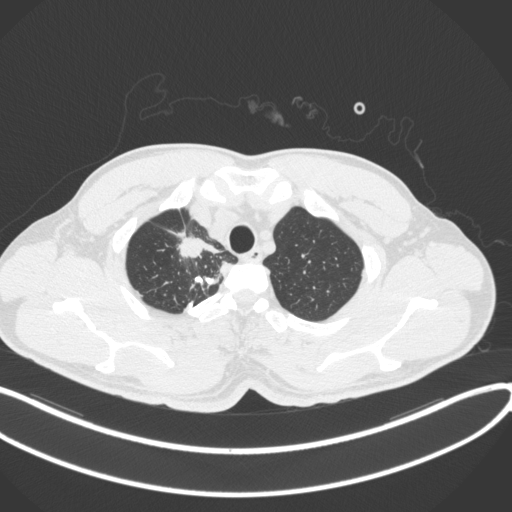
Chest CT, one axial slice. Slice 329 of 391 in the series (ordered by position). Reconstruction kernel B31f. Lung window (W 1500 / L -600 HU). 512 × 512 image matrix, field of view 400 × 400 mm. Male patient, age 48 years. Case-level facts recorded for this patient, not image findings: clinical TNM (as recorded): T1c N1 M1.
Outlined on this slice (bounding box drawn by a radiologist):
- lung tumour (recorded histology: adenocarcinoma): bounding box [x1, y1, x2, y2] px = [177, 232, 223, 261]